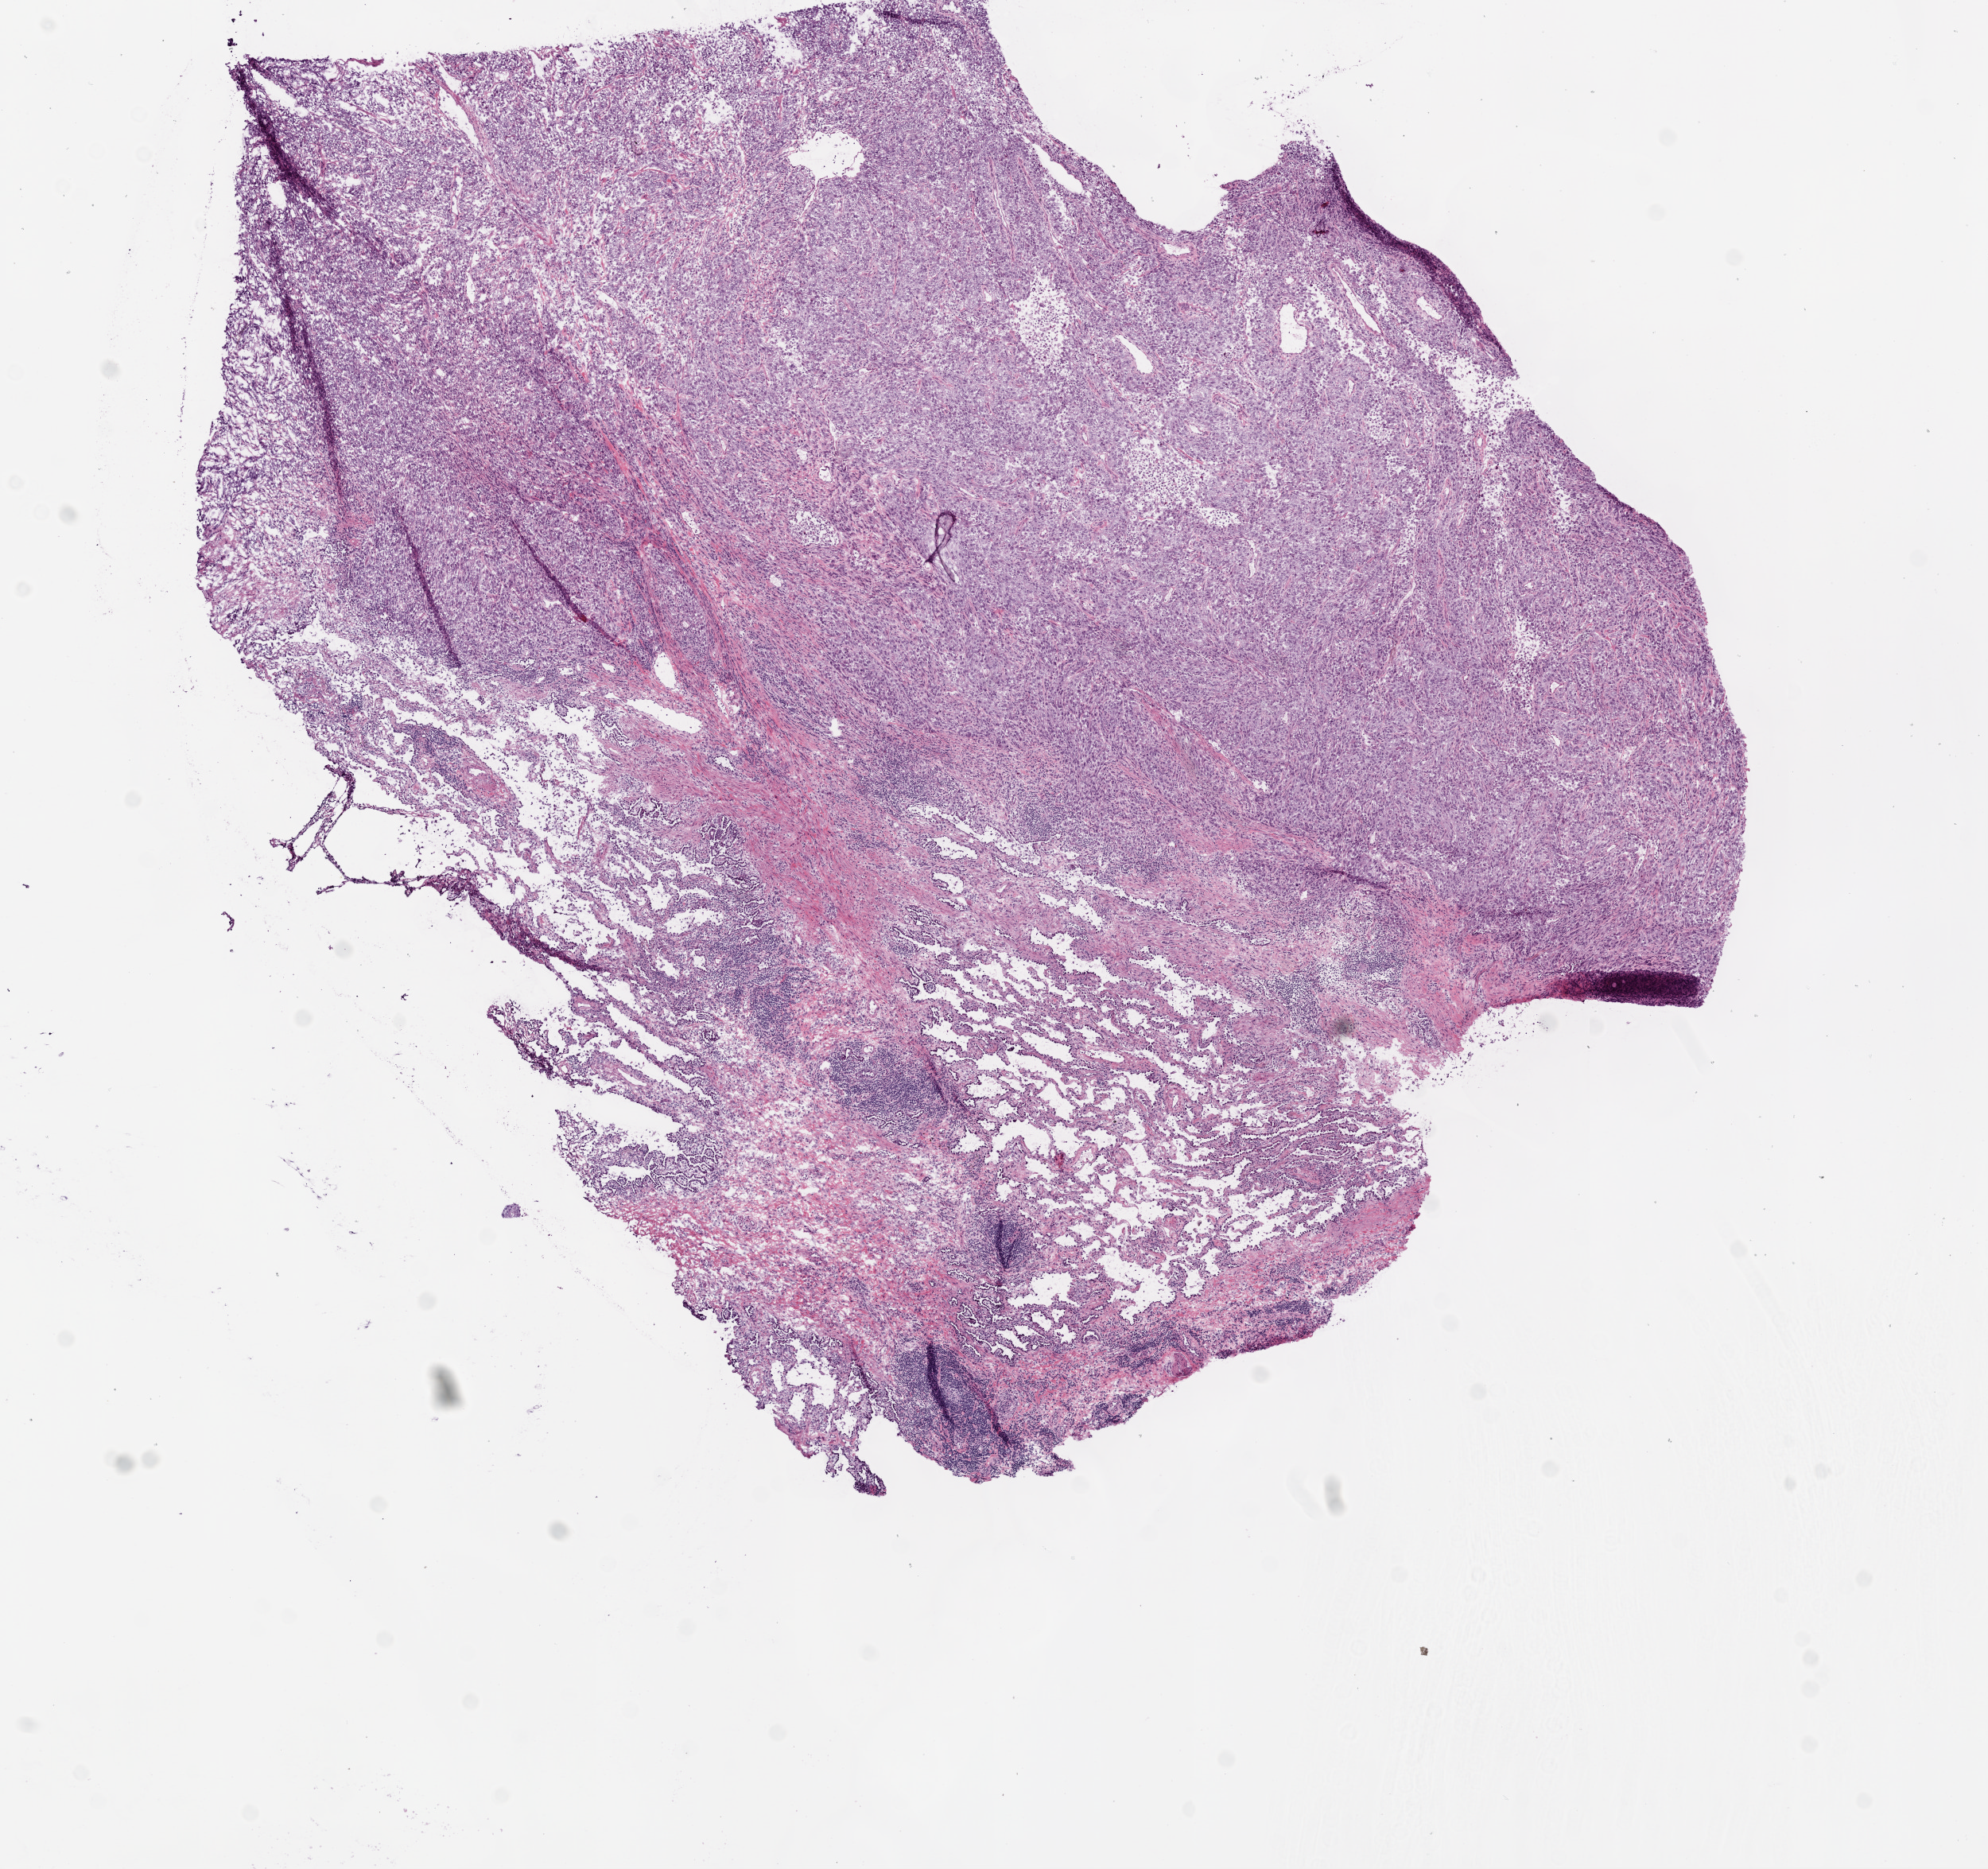
Digitized H&E tissue section (whole slide), a low-resolution overview of the entire scanned area, about 10.0 x 9.4 mm. Frozen section from the bottom of the tissue portion. Primary tumour sample from the lung. Female patient; age at initial diagnosis 66 years. Slide review estimates, as recorded: tumour cells 73%, tumour nuclei 75%, normal cells 20%, stromal cells 2%, necrosis 5%.
- histologic diagnosis: Adenocarcinoma, NOS (upper lobe, lung)
- TNM: T2a N0 M0
- AJCC pathologic stage: IB (5th edition)